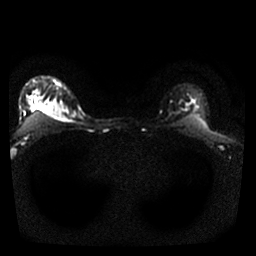
Breast MRI, one axial slice. Position 25 of 25 along the scan axis. Diffusion-weighted series; image 2 of 4 stored at this slice position (different b-values; order by instance number). 1.5 T. 256 × 256 image matrix. Female patient.
Structures marked on this image (expert manual segmentation):
- tumour on diffusion-weighted imaging: bounding box (x1, y1, x2, y2) in pixels: (41, 102, 64, 118)